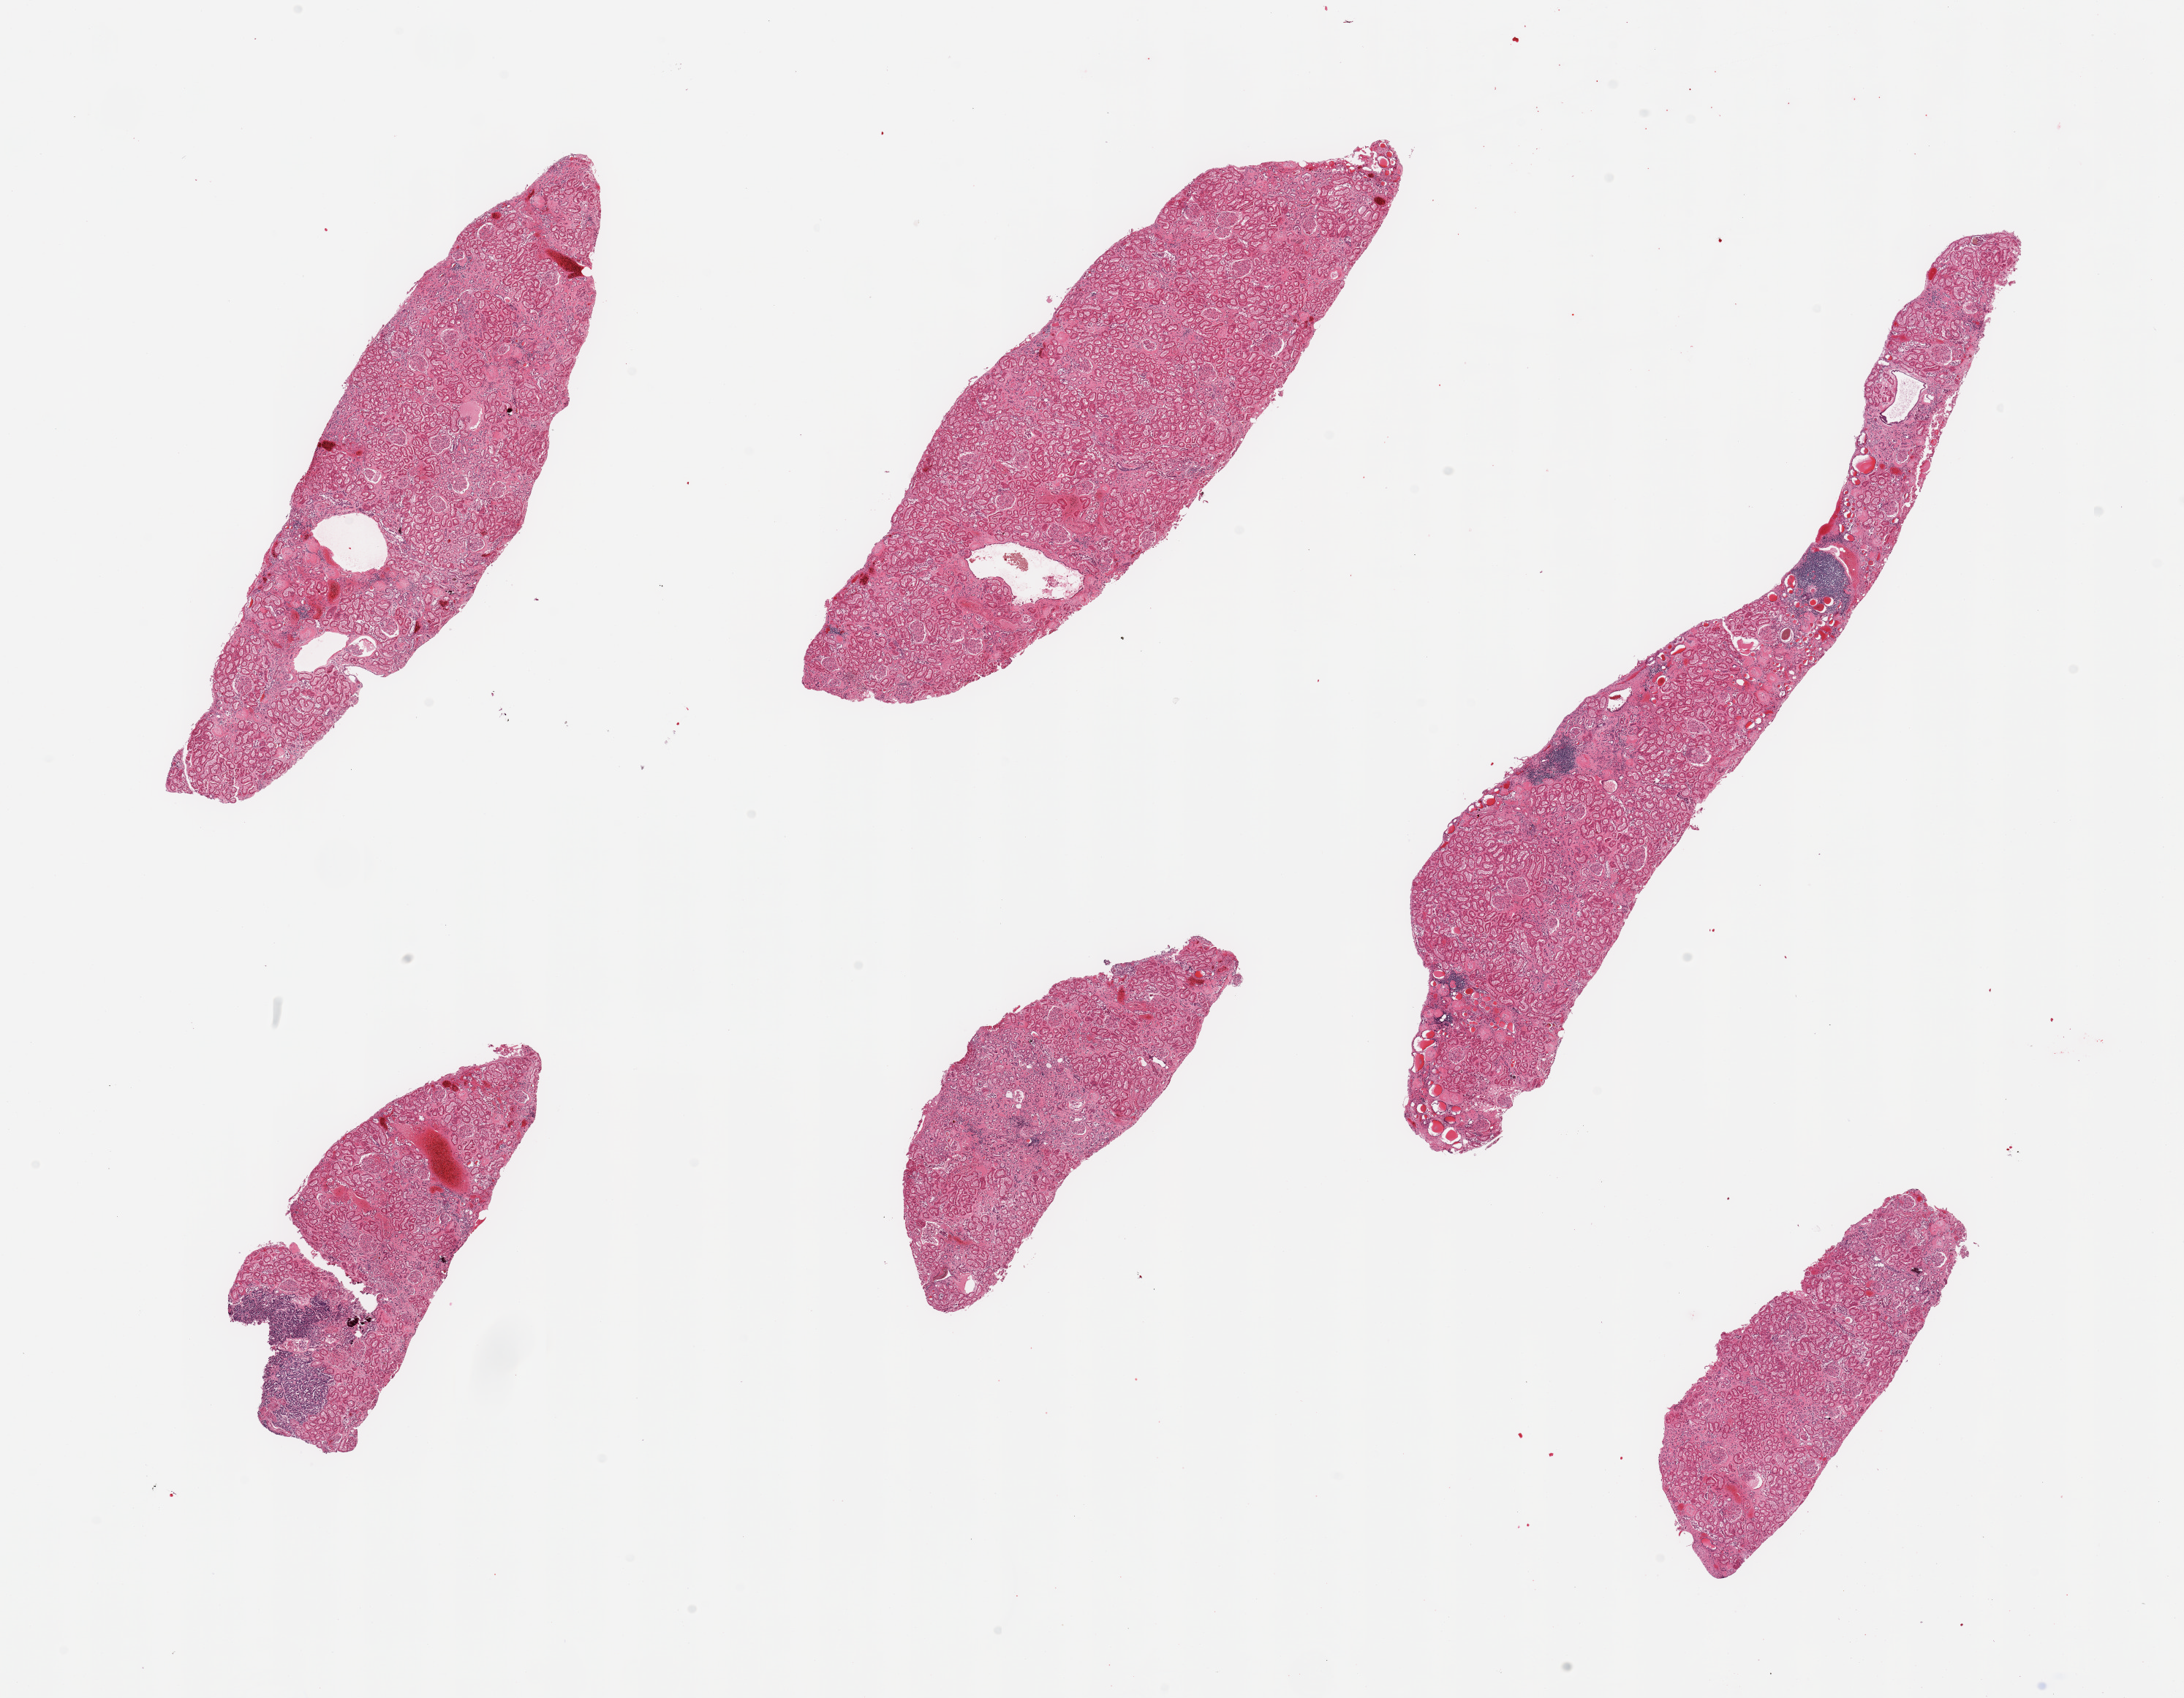
Digitized haematoxylin and eosin-stained section, brightfield, low-resolution overview of the scanned area, about 23.6 x 18.4 mm (from a 20x scan); PAXgene-fixed paraffin-embedded (PFPE) section; target tissue: renal cortex; donor tissue sample. Donor: male.
Reviewer comment on this tissue sample: 6 pieces, glomeruli present; moderate-severe chronic glomeruo and tubular nephritis with focal thyroidization, interstitial fibrosis.